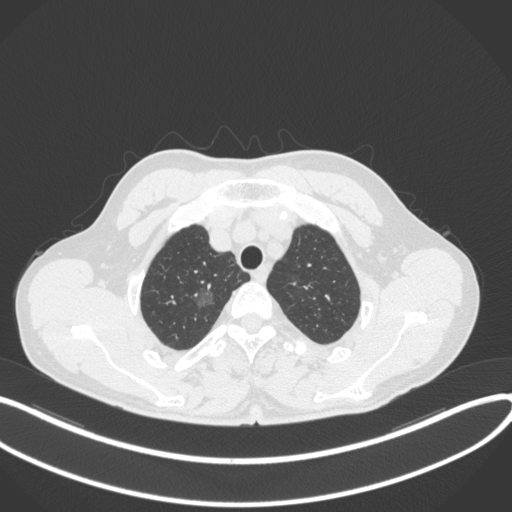
Chest CT, one axial slice; position 322 of 407 along the scan axis; reconstruction kernel B31f; 120 kVp; lung window (W 1500 / L -600 HU); 1 mm slice thickness; 512 × 512 image matrix, field of view 400 × 400 mm. Patient: male, 58 years. From the clinical record (not read from this slice): clinical TNM (as recorded): T1c N0 M0; histopathological grade: G1-2.
Outlined on this slice (bounding box drawn by a radiologist):
- lung tumour (recorded histology: adenocarcinoma): box from (x=187, y=282) to (x=216, y=313) px